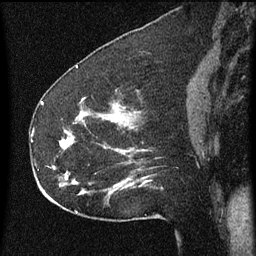
Breast MRI (dynamic contrast-enhanced), one sagittal slice; position 25 of 60 along the scan axis; dynamic contrast-enhanced series, image 2 of 3 at this slice position (ordered by acquisition); 1.5 T; TE 4.2 ms, TR 8 ms; 2 mm slice thickness; 256 × 256 image matrix, field of view 180 × 180 mm. Patient: female, 52 years.
Annotated regions visible in this slice (semi-automatically segmented with operator editing):
- analysis volume of interest (the breast-tissue region the enhancement analysis was run in; not a lesion): box from (x=54, y=110) to (x=161, y=207) px
- tumour enhancement mask (voxels above the 70 % enhancement threshold inside the analysis volume of interest): (x=59, y=120)–(x=147, y=193)